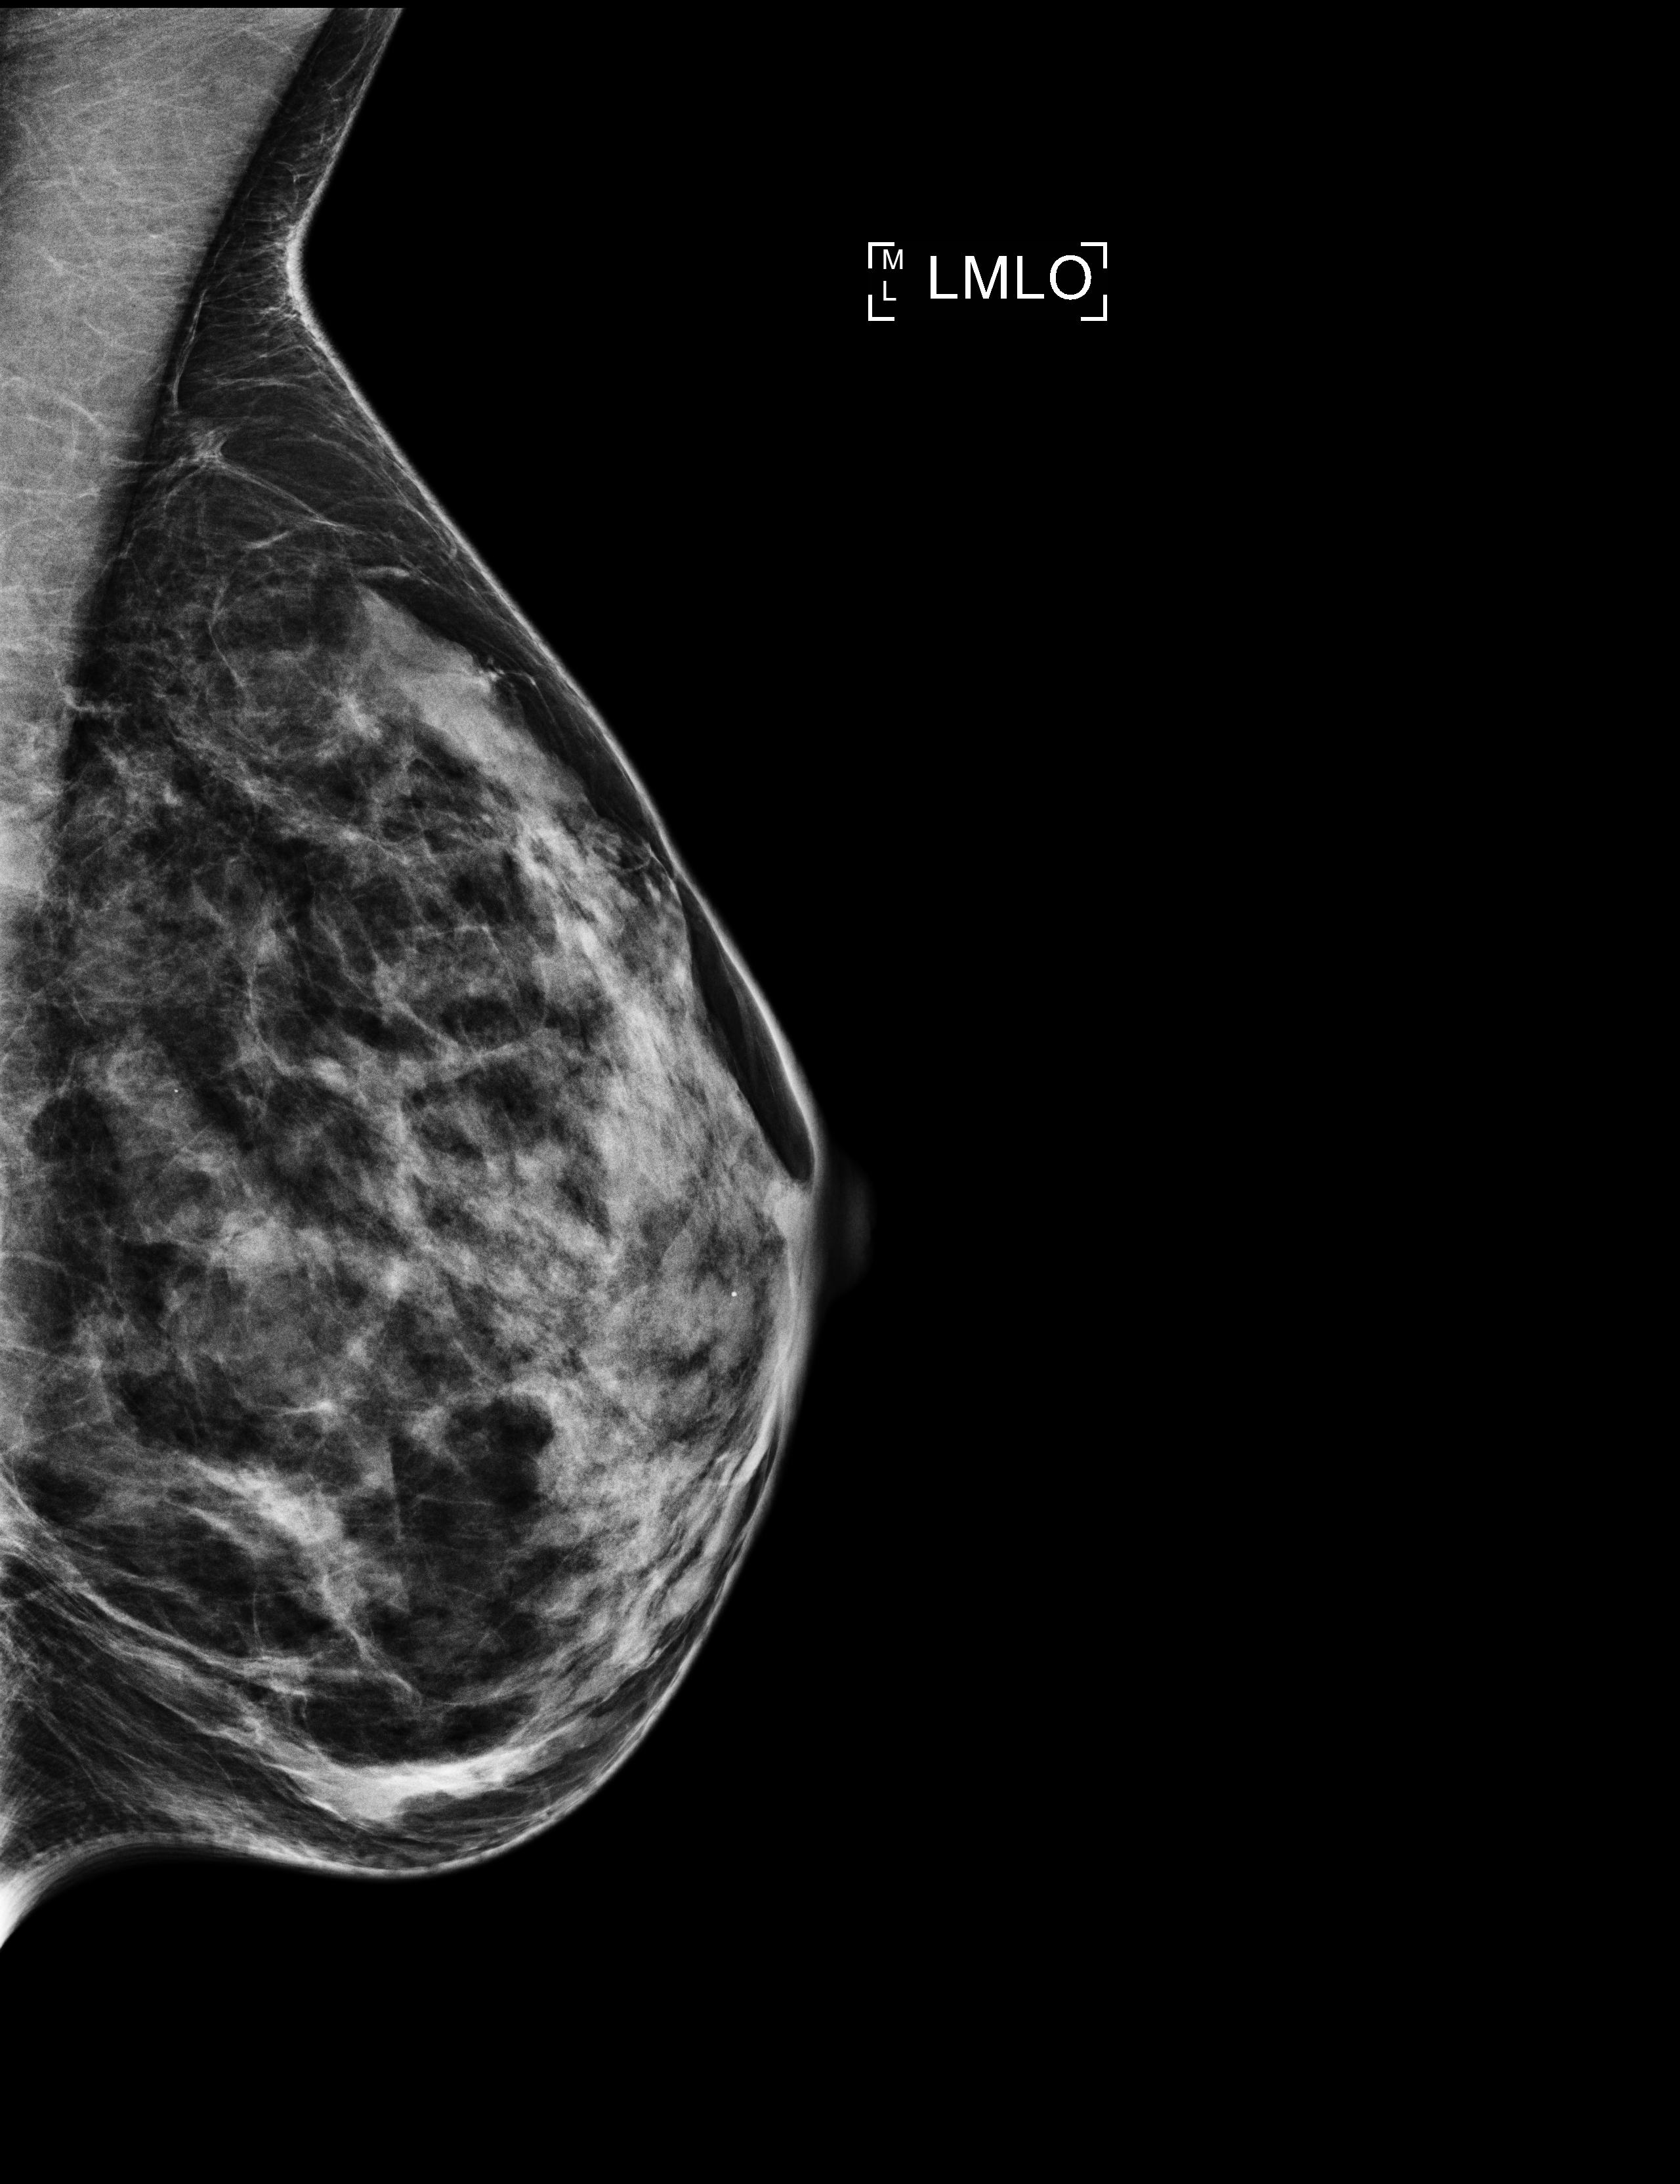
Full-field digital mammogram (FFDM), left breast, medio-lateral oblique projection, annual screening mammography examination, system: Selenia Dimensions. Patient: female, 52 years.
- BI-RADS breast density category at the screening exam (both breasts, scale 1–4): 3
- final BI-RADS category for the screening round (tomosynthesis exam, both breasts): category 2
- recall: no recall after this screen